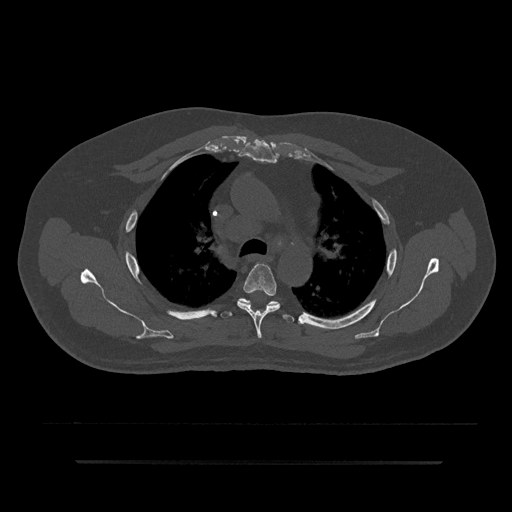
CT including the spine, one axial slice. Position 608 of 797 along the scan axis. 120 kVp. Bone window (W 1800 / L 400 HU). 0.5 mm slice thickness. 512 × 512 image matrix, field of view 464 × 464 mm. Male patient, age 59 years. Case-level facts recorded for this patient, not image findings: primary cancer: bile ducts; vertebrae with lytic lesions (as recorded): T10.
Annotated regions visible in this slice (semi-automatically segmented with operator editing):
- T4 vertebra: bounding box (x1, y1, x2, y2) in pixels: (237, 263, 280, 339)
- T5 vertebra: (221, 298, 294, 322)